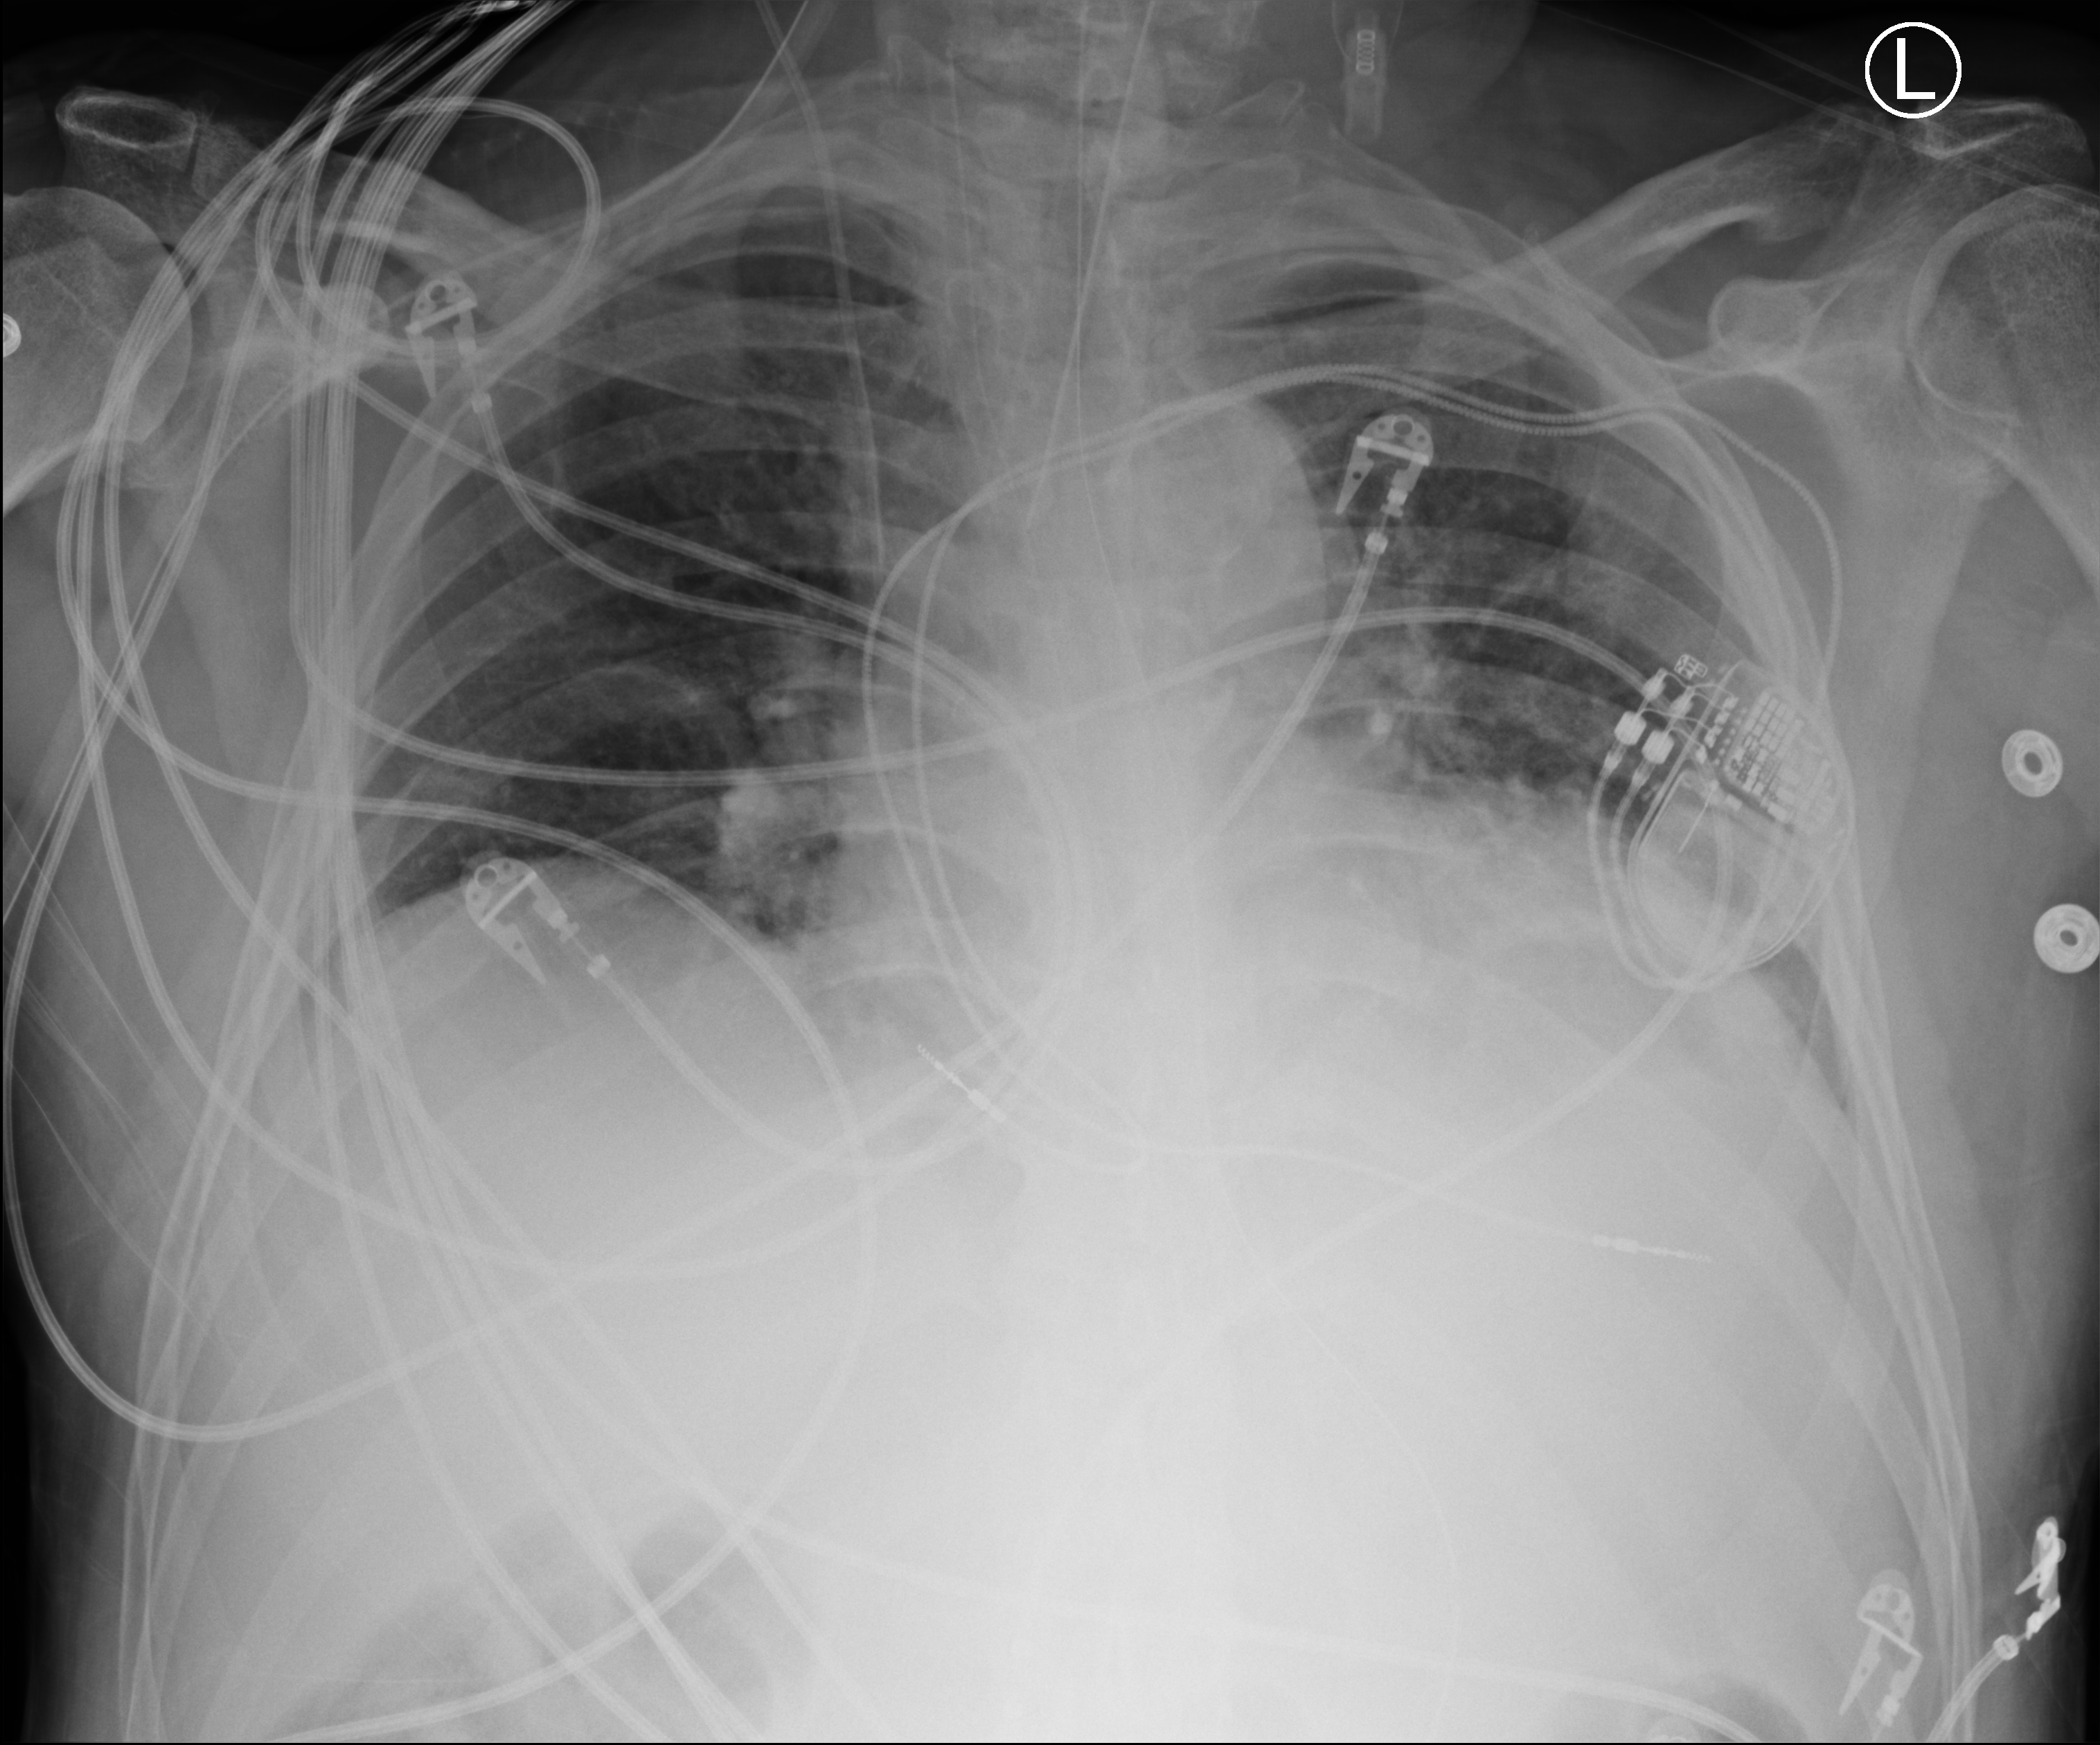
Chest X-ray (portable). Male patient hospitalised with COVID-19, age 60–74 years.
From the hospital-stay record, not from the radiograph (when in the stay this image was taken is not recorded): admitted to intensive care during this hospital stay: yes; mechanically ventilated during this hospital stay: yes; length of hospital stay: 41 days.